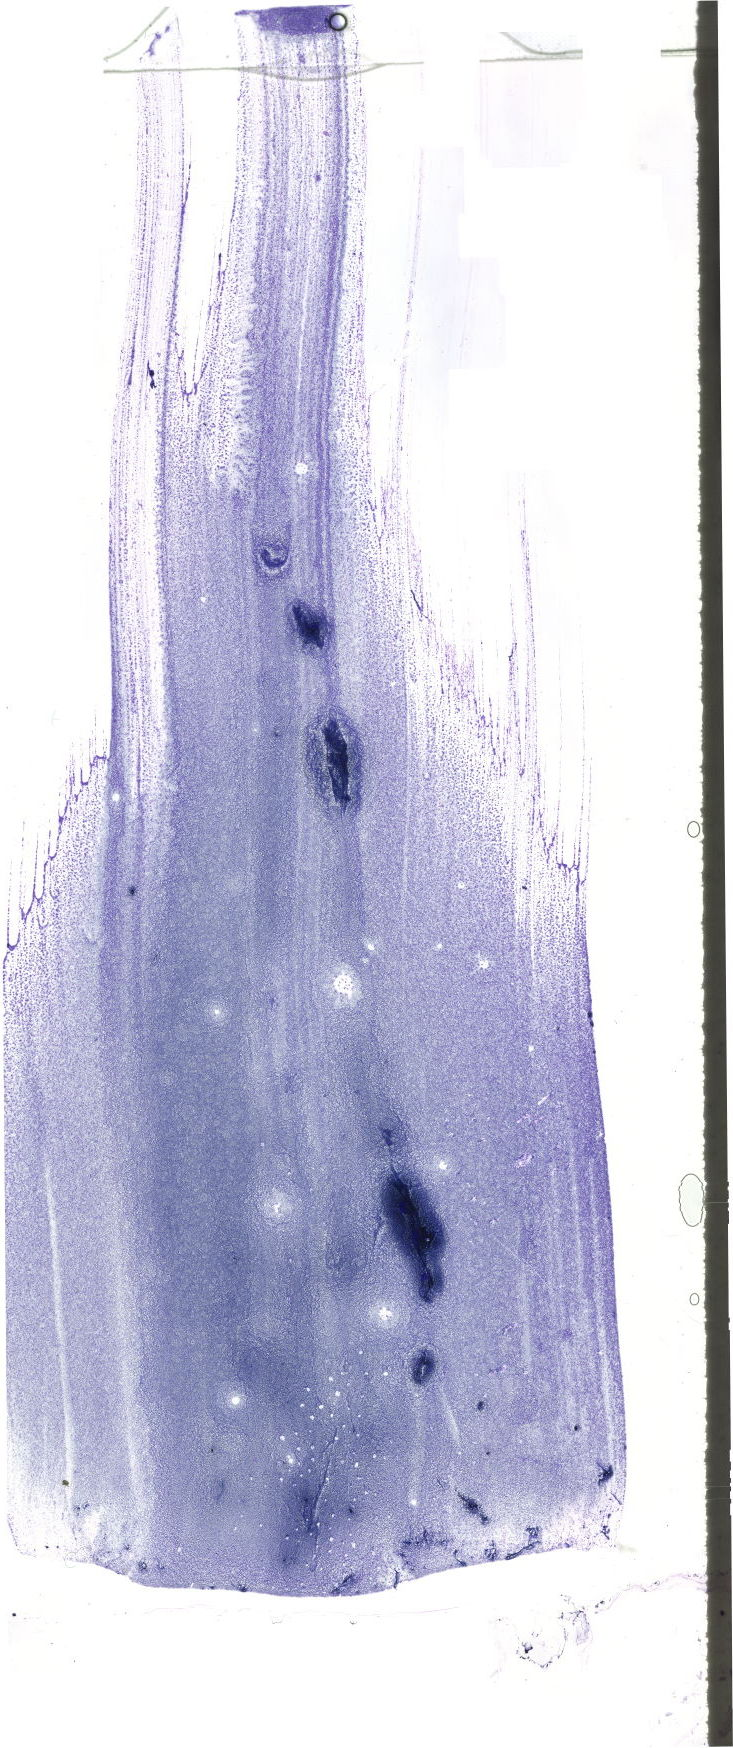
Whole-slide image of a May-Grünwald-Giemsa (MGG)-stained bone marrow aspirate smear, shown as a low-resolution overview of the whole scanned area (about 20.8 x 49.5 mm). Male patient.
* diagnosis: Blast Phase Chronic Myeloid Leukemia, BCR-ABL1 Positive